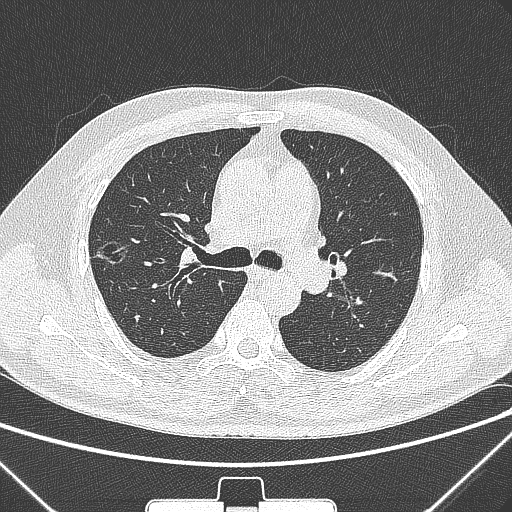
Chest CT, one axial slice. Lung window (W 1500 / L -600 HU). 1 mm slice thickness. 512 × 512 image matrix, field of view 350 × 350 mm. Male patient, age 58 years. Case-level facts recorded for this patient, not image findings: clinical TNM (as recorded): T1c N0 M0.
Outlined on this slice (bounding box drawn by a radiologist):
- lung tumour (recorded histology: adenocarcinoma): bounding box (x1, y1, x2, y2) in pixels: (90, 229, 133, 277)